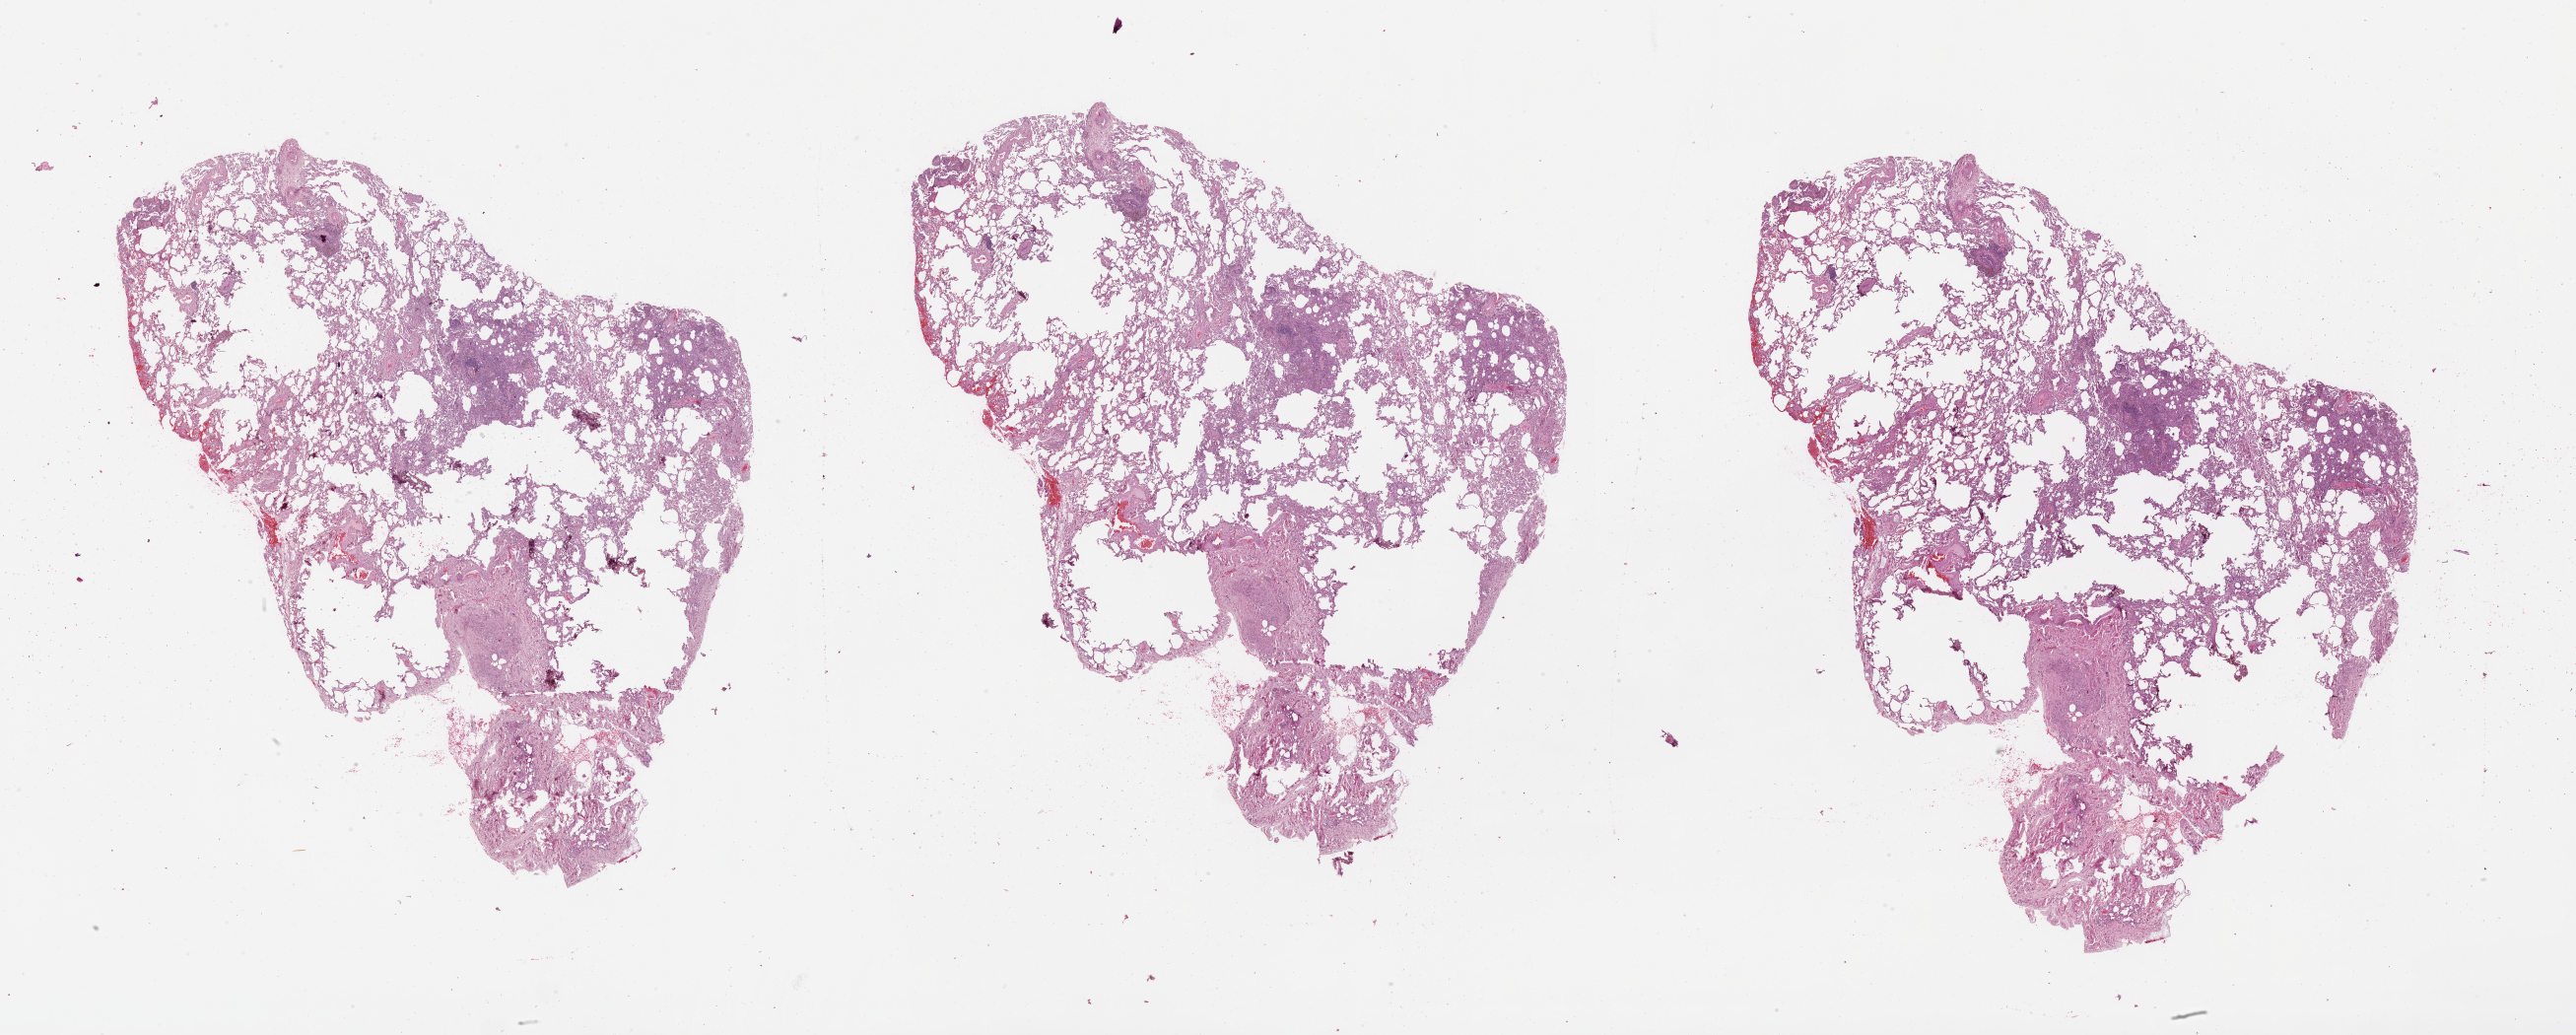
Digitized H&E-stained tissue section (whole slide) — shown as a low-resolution overview of the whole scanned area (about 42.1 x 16.9 mm, acquisition: 20x scan); normal (non-tumour) tissue sample, lung. Patient: male, age 43 years.
• this section: normal (non-tumour) tissue from the same patient
• patient diagnosis (cohort enrolment): squamous cell carcinoma (lung)